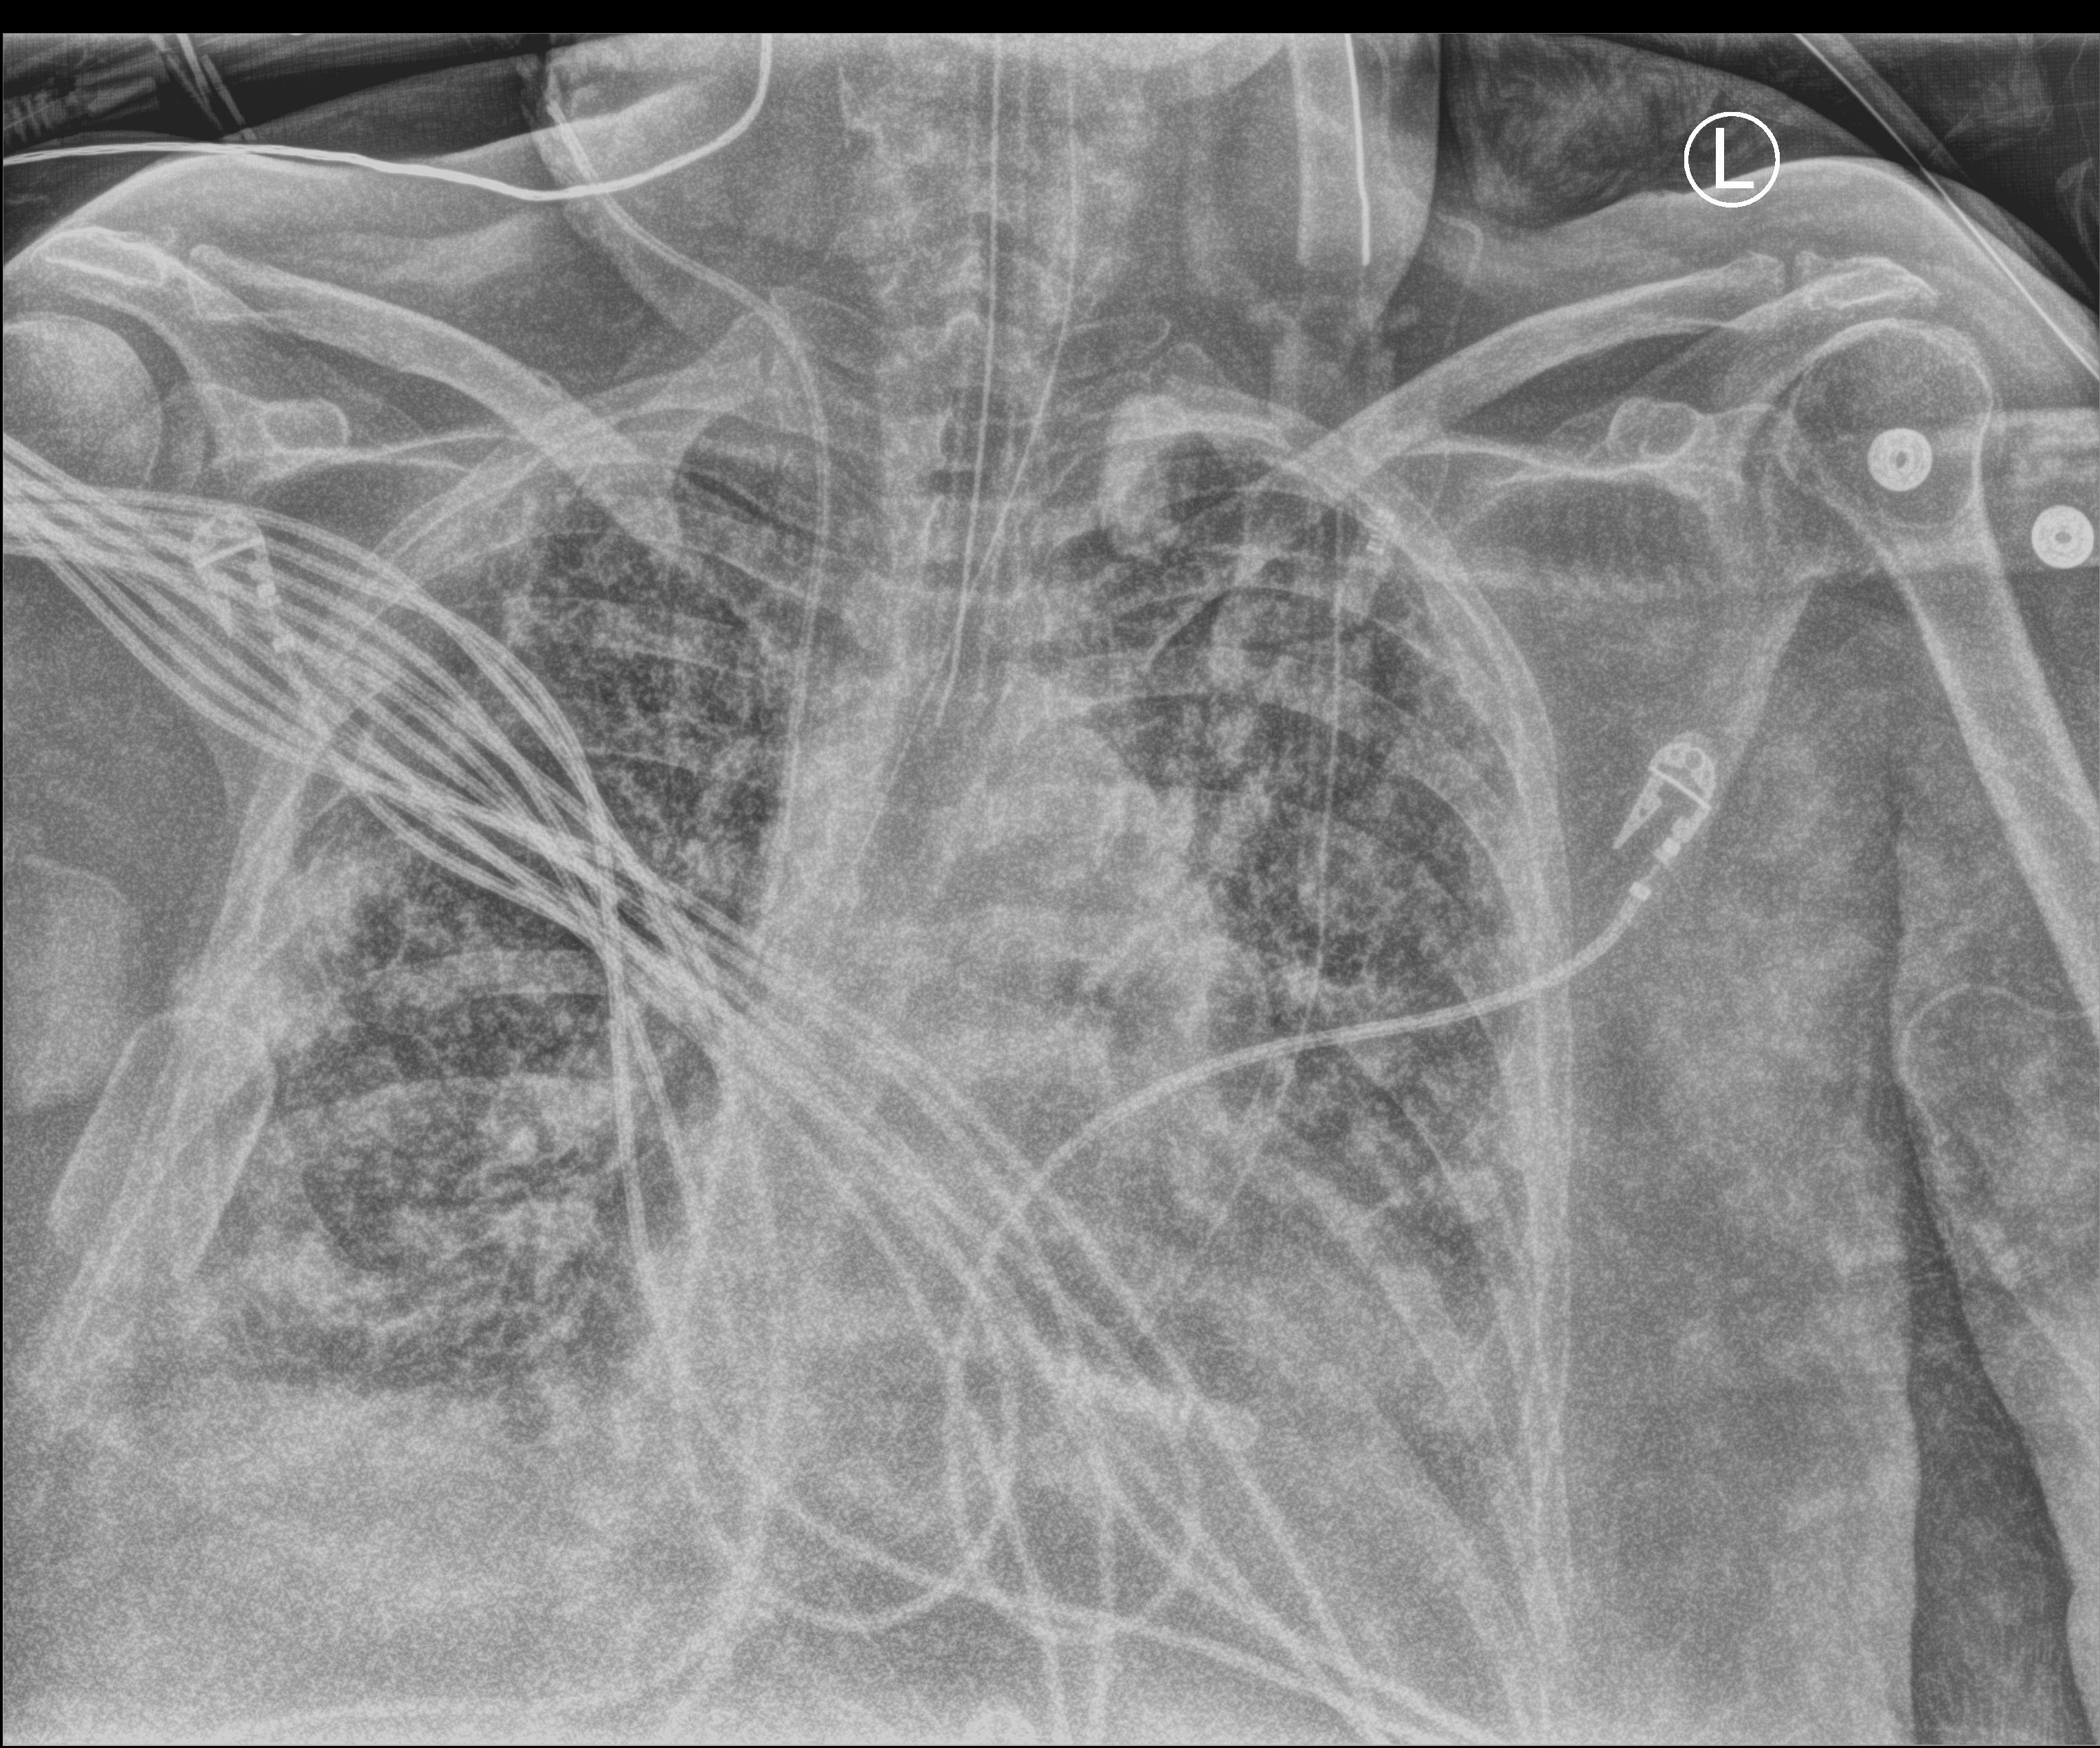
Portable chest radiograph, anteroposterior (AP) projection. Patient hospitalised with COVID-19; female, aged 60–74 years.
Hospital-stay facts (about this admission, not read from this image; timing relative to this image not recorded):
- diabetes (admission record): yes
- length of hospital stay: 28 days
- admitted to intensive care during this hospital stay: yes